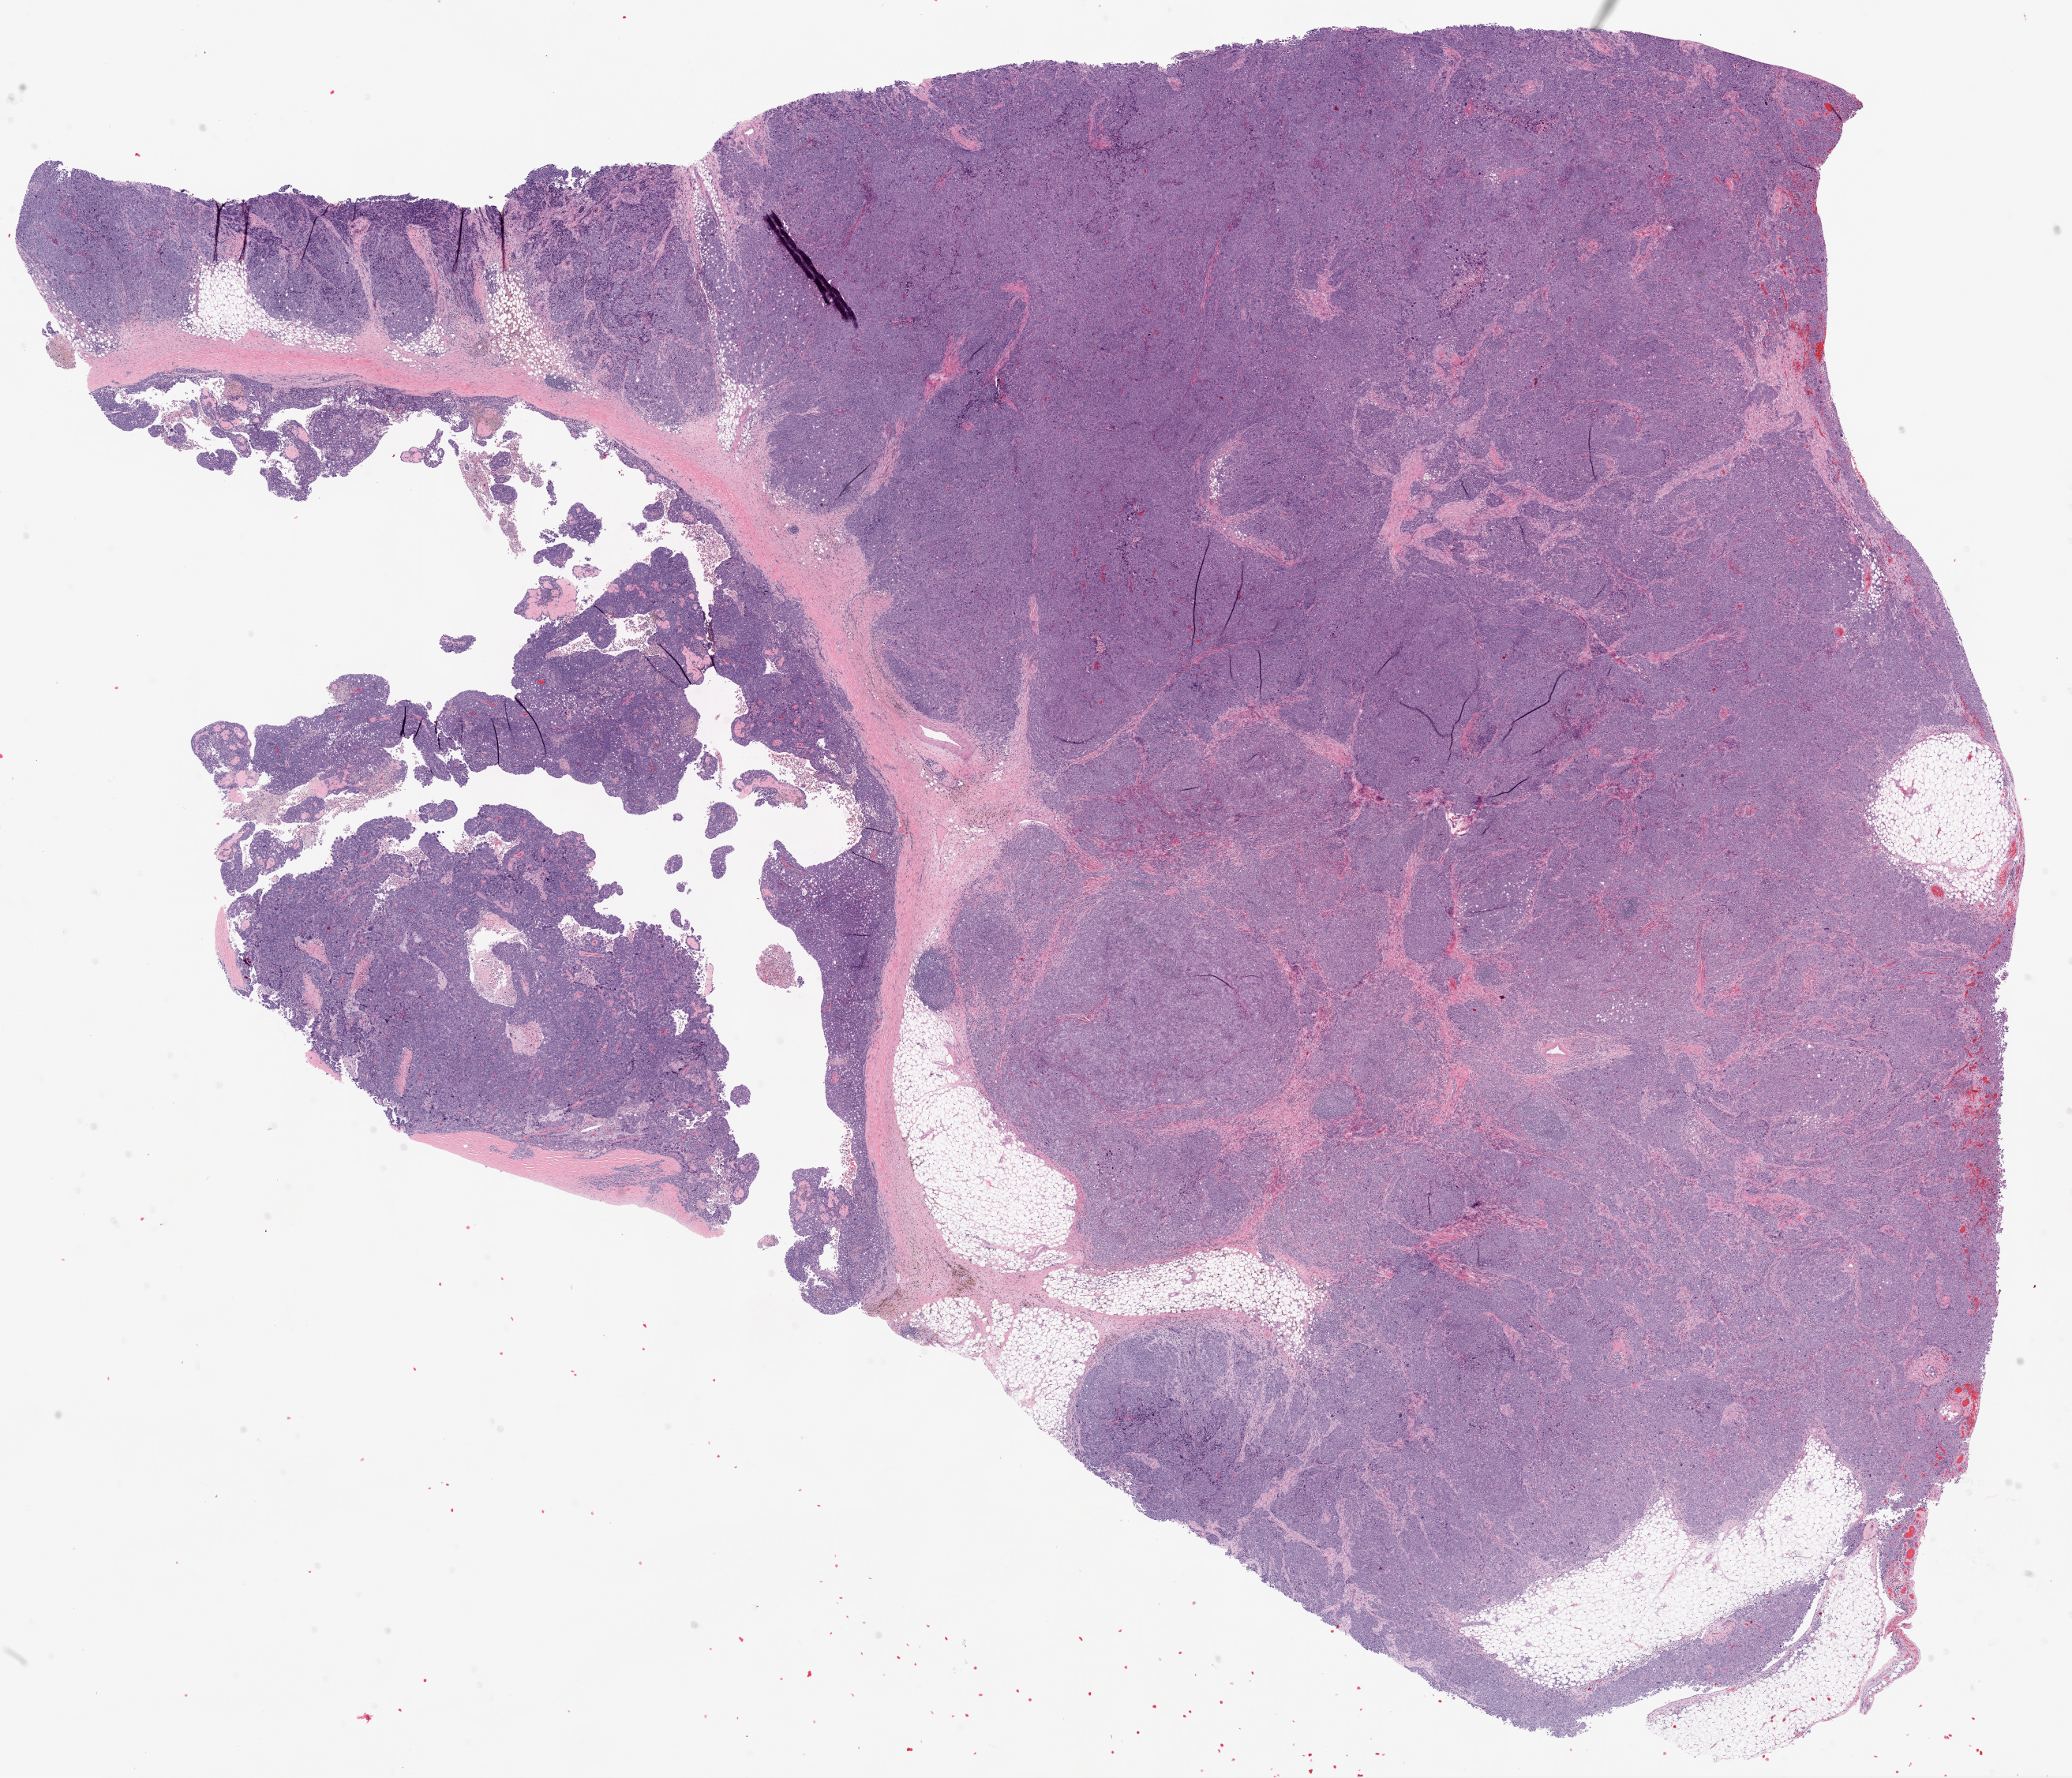
Digitized H&E tissue section (whole slide), low-resolution overview of the scanned area, about 21.1 x 18.1 mm (slide scanned at 20x). Frozen section from the top of the tissue portion. Sample: primary tumour, ovary. Female, age 85 years at initial diagnosis.
Diagnosis: Serous cystadenocarcinoma, NOS.